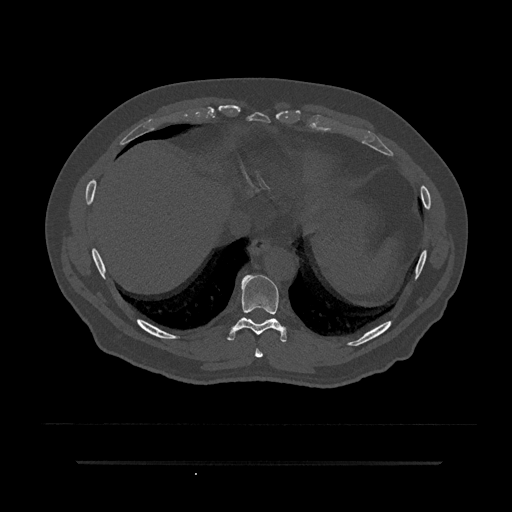
CT including the spine, one axial slice. Slice 375 of 797 in the series (ordered by position). Reconstruction kernel Br40s/3. 120 kVp. Bone window (W 1800 / L 400 HU). 512 × 512 image matrix, field of view 464 × 464 mm. Male patient, age 59 years. Case-level facts recorded for this patient, not image findings: primary cancer: bile ducts.
Annotated regions visible in this slice (semi-automatically segmented with operator editing):
- T8 vertebra: bounding box (x1, y1, x2, y2) in pixels: (255, 348, 263, 358)
- T9 vertebra: (227, 275, 287, 342)